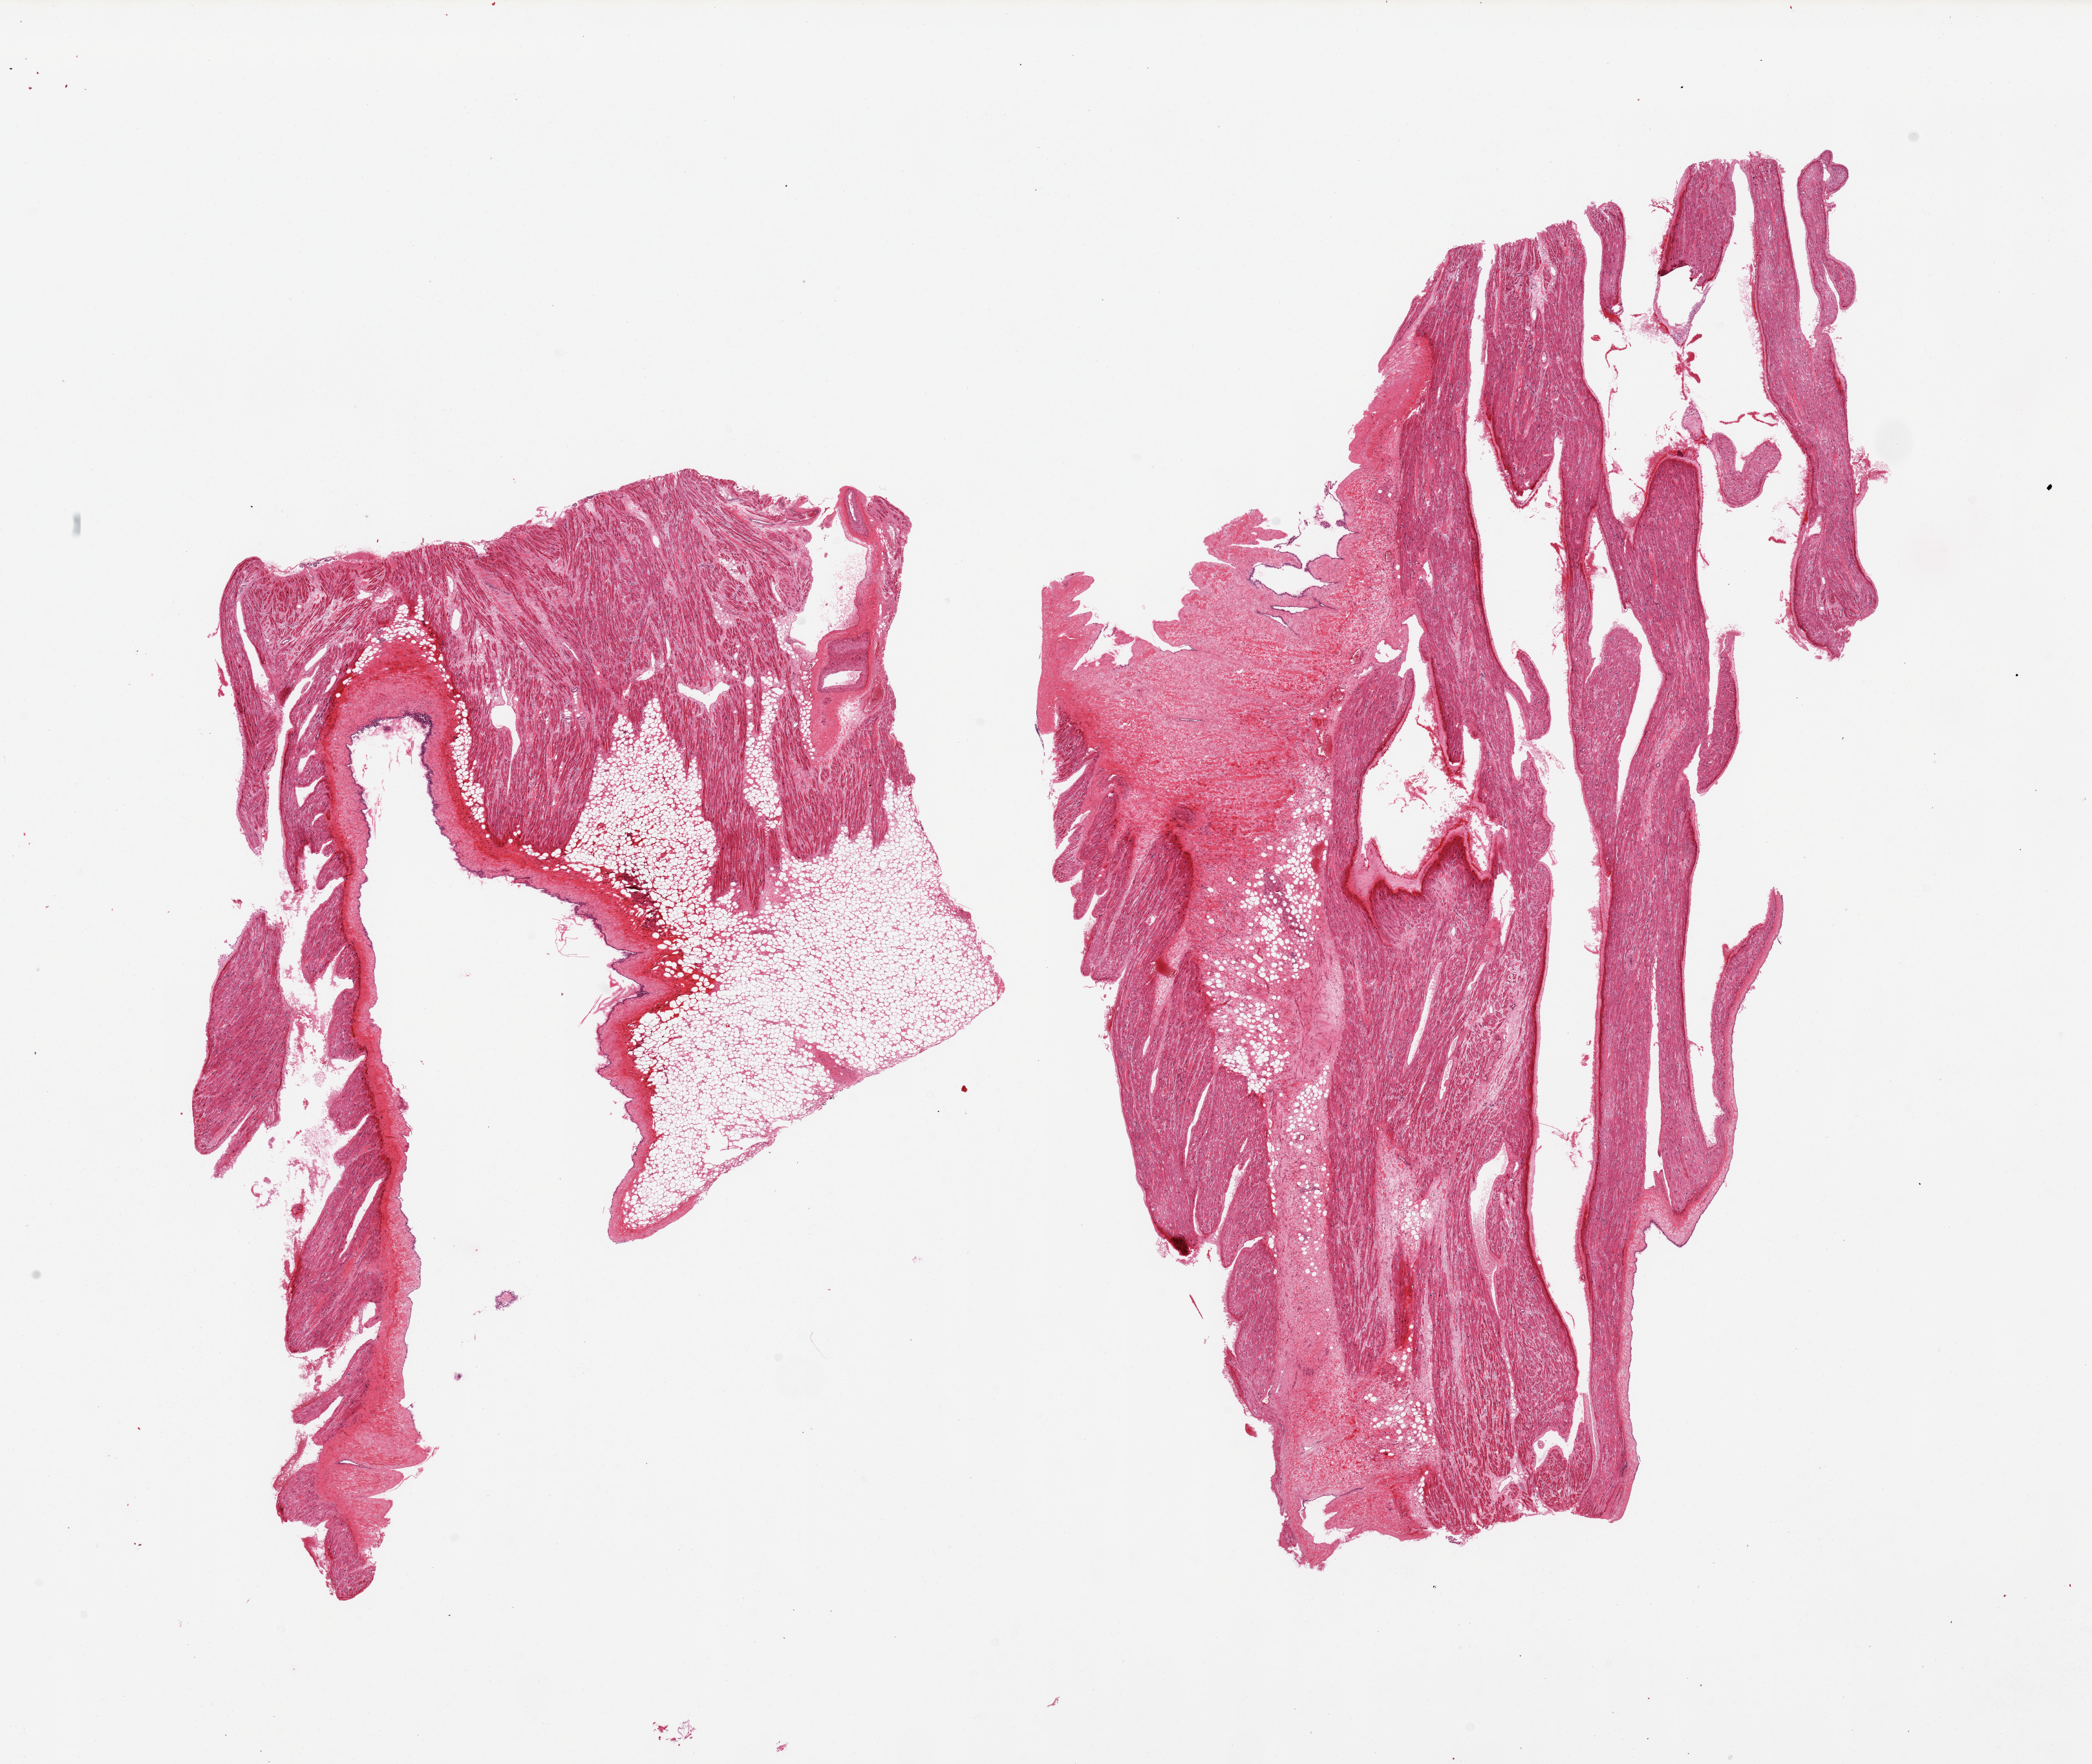
Whole-slide image, hematoxylin and eosin (H&E) stain — low-resolution overview of the scanned area, about 25.6 x 21.6 mm, PAXgene-fixed paraffin-embedded (PFPE) section, section of auricular appendage (target tissue), donor tissue sample. Donor sex: female.
Reviewer comment on this tissue sample: 2 pieces; 1 has 60% fat, other has 30% fibroadipose tissue.